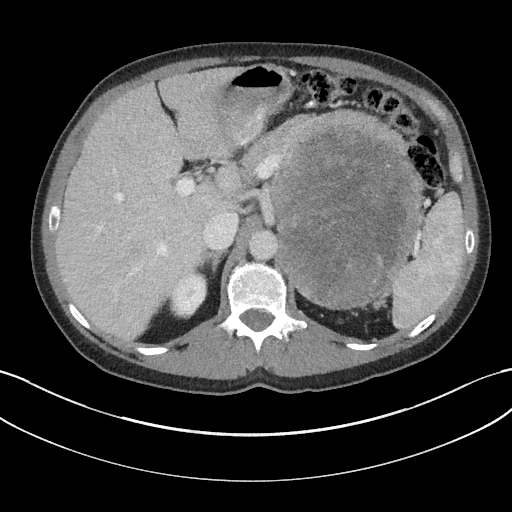
Contrast-enhanced abdominal CT, one axial slice. Slice 117 of 147 in the series (ordered by position). Reconstruction kernel I31f/3. Intravenous contrast given. Soft-tissue window (W 400 / L 40 HU). 512 × 512 image matrix. Patient: male, 58 years. From the clinical record (not read from this slice): diagnosis: adrenocortical carcinoma; tumour side: left adrenal; tumour size at pathology: 22 cm; Ki-67 index: 26 %; stage (as recorded): 2.
Structures marked on this image (semi-automatically segmented with operator editing):
- mass: bounding box <274,135,415,306> (left, top, right, bottom; pixels)